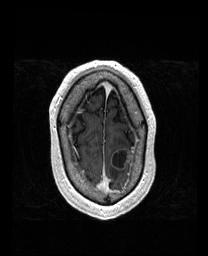
Brain MRI from a brain-tumour surgery series, one axial slice; position 152 of 192 along the scan axis; T1-weighted post-contrast; 1 mm slice thickness; 208 × 256 image matrix. Case-level facts recorded for this patient, not image findings: histopathology: Metastatic Carcinoma from Lung Adenocarcinoma.
Annotated regions visible in this slice (outlined manually by an expert reader):
- tumour: bounding box <113,148,131,168> (left, top, right, bottom; pixels)